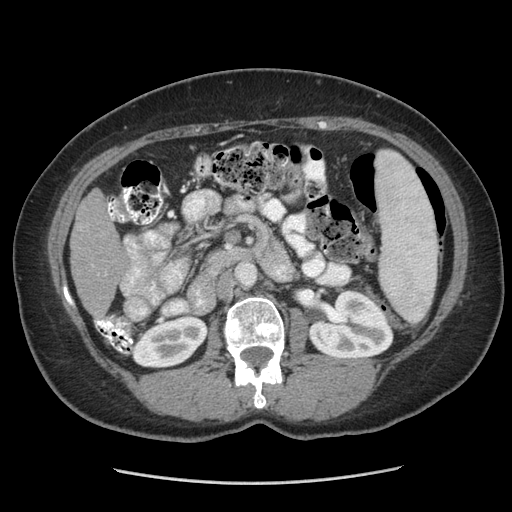
Contrast-enhanced abdominal CT (liver protocol), one axial slice; slice 123 of 185 in the series (ordered by position); reconstruction kernel STANDARD; 140 kVp; soft-tissue window (W 400 / L 40 HU); 2.5 mm slice thickness; 512 × 512 image matrix, field of view 360 × 360 mm. Case-level facts recorded for this patient, not image findings: diagnosis: hepatocellular carcinoma (patient treated with transarterial chemoembolisation; whether this scan precedes or follows treatment is not stated here); TNM stage (as recorded): Stage-I; Child-Pugh class: A; tumour differentiation: poorly differentiated; tumour nodularity: uninodular.
Structures marked on this image (semi-automatically segmented with operator editing):
- liver parenchyma outside the tumour (the mass and vessels are separate outlines, so this box may not span the whole liver): bounding box <70,188,128,316> (left, top, right, bottom; pixels)